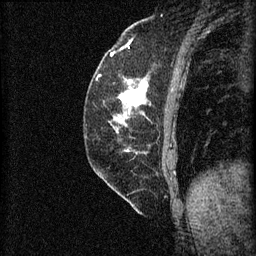
Breast MRI (dynamic contrast-enhanced), one sagittal slice; position 22 of 60 along the scan axis; 3 images stored at this slice position (order not interpretable as contrast timing); 1.5 T; TE 4.2 ms, TR 8.2 ms; 2 mm slice thickness; 256 × 256 image matrix, field of view 180 × 180 mm. Female patient, age 59 years.
Annotated regions visible in this slice (semi-automatically segmented with operator editing):
- analysis volume of interest (the breast-tissue region the enhancement analysis was run in; not a lesion): bounding box (x1, y1, x2, y2) in pixels: (94, 74, 152, 131)
- tumour enhancement mask (voxels above the 70 % enhancement threshold inside the analysis volume of interest): (119, 80, 149, 111)